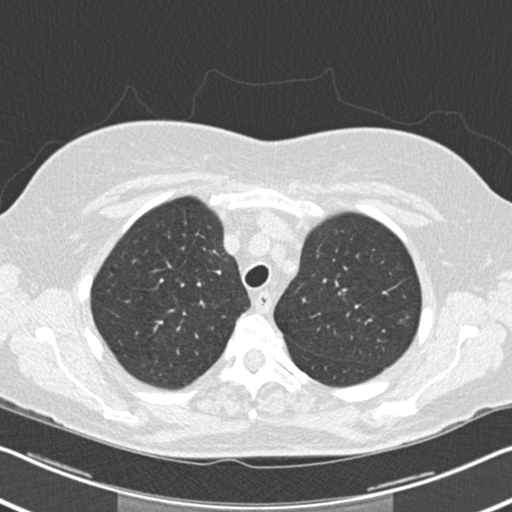
Chest CT (low-dose screening protocol), one axial image. Second screening round (one year after baseline). Lung window (W 1500 / L -600 HU). Standard (soft-tissue) reconstruction kernel (B30f). Slice 46 of 202 in the series. 512 × 512 image matrix. Female participant, aged 60 years at enrolment. Current smoker at enrolment.
Expert reader's lesion annotation, box from (x=388, y=305) to (x=426, y=341) px. The screening reader recorded 6 non-calcified nodules or masses ≥4 mm on this exam (right upper lobe, right middle lobe, right lower lobe, right lower lobe, left lower lobe, lingula); which of them this box marks is not recorded. Later outcome: lung cancer diagnosed 495 days after this screen — non-small cell carcinoma, left upper lobe, poorly differentiated (G3), stage IB (AJCC 6th edition), 7 mm at pathology.